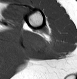
MRI of an extremity soft-tissue mass, one axial slice; position 6 of 28 along the scan axis; MR volume resampled by the dataset authors to the PET/CT grid (not the native acquisition matrix); 3.27 mm slice thickness; 77 × 79 image matrix, field of view 75 × 77 mm. Female patient. From the clinical record (not read from this slice): histological type: malignant fibrous histiocytoma; grade: low; site of the primary tumour: left arm.
Outlined on this slice (expert contour drawn on MRI and transferred to this co-registered scan by the dataset authors):
- gross tumour volume (mass): box from (x=35, y=36) to (x=54, y=55) px